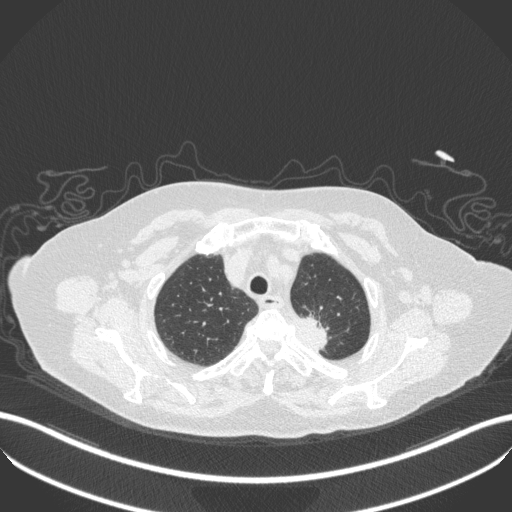
Chest CT, one axial slice. Position 287 of 353 along the scan axis. Reconstruction kernel B31f. Lung window (W 1500 / L -600 HU). 1 mm slice thickness. 512 × 512 image matrix, field of view 400 × 400 mm. Female patient, age 81 years. Case-level facts recorded for this patient, not image findings: clinical TNM (as recorded): T2a N0 M0.
Annotated regions visible in this slice (bounding box drawn by a radiologist):
- lung tumour (recorded histology: adenocarcinoma): box from (x=287, y=313) to (x=344, y=358) px